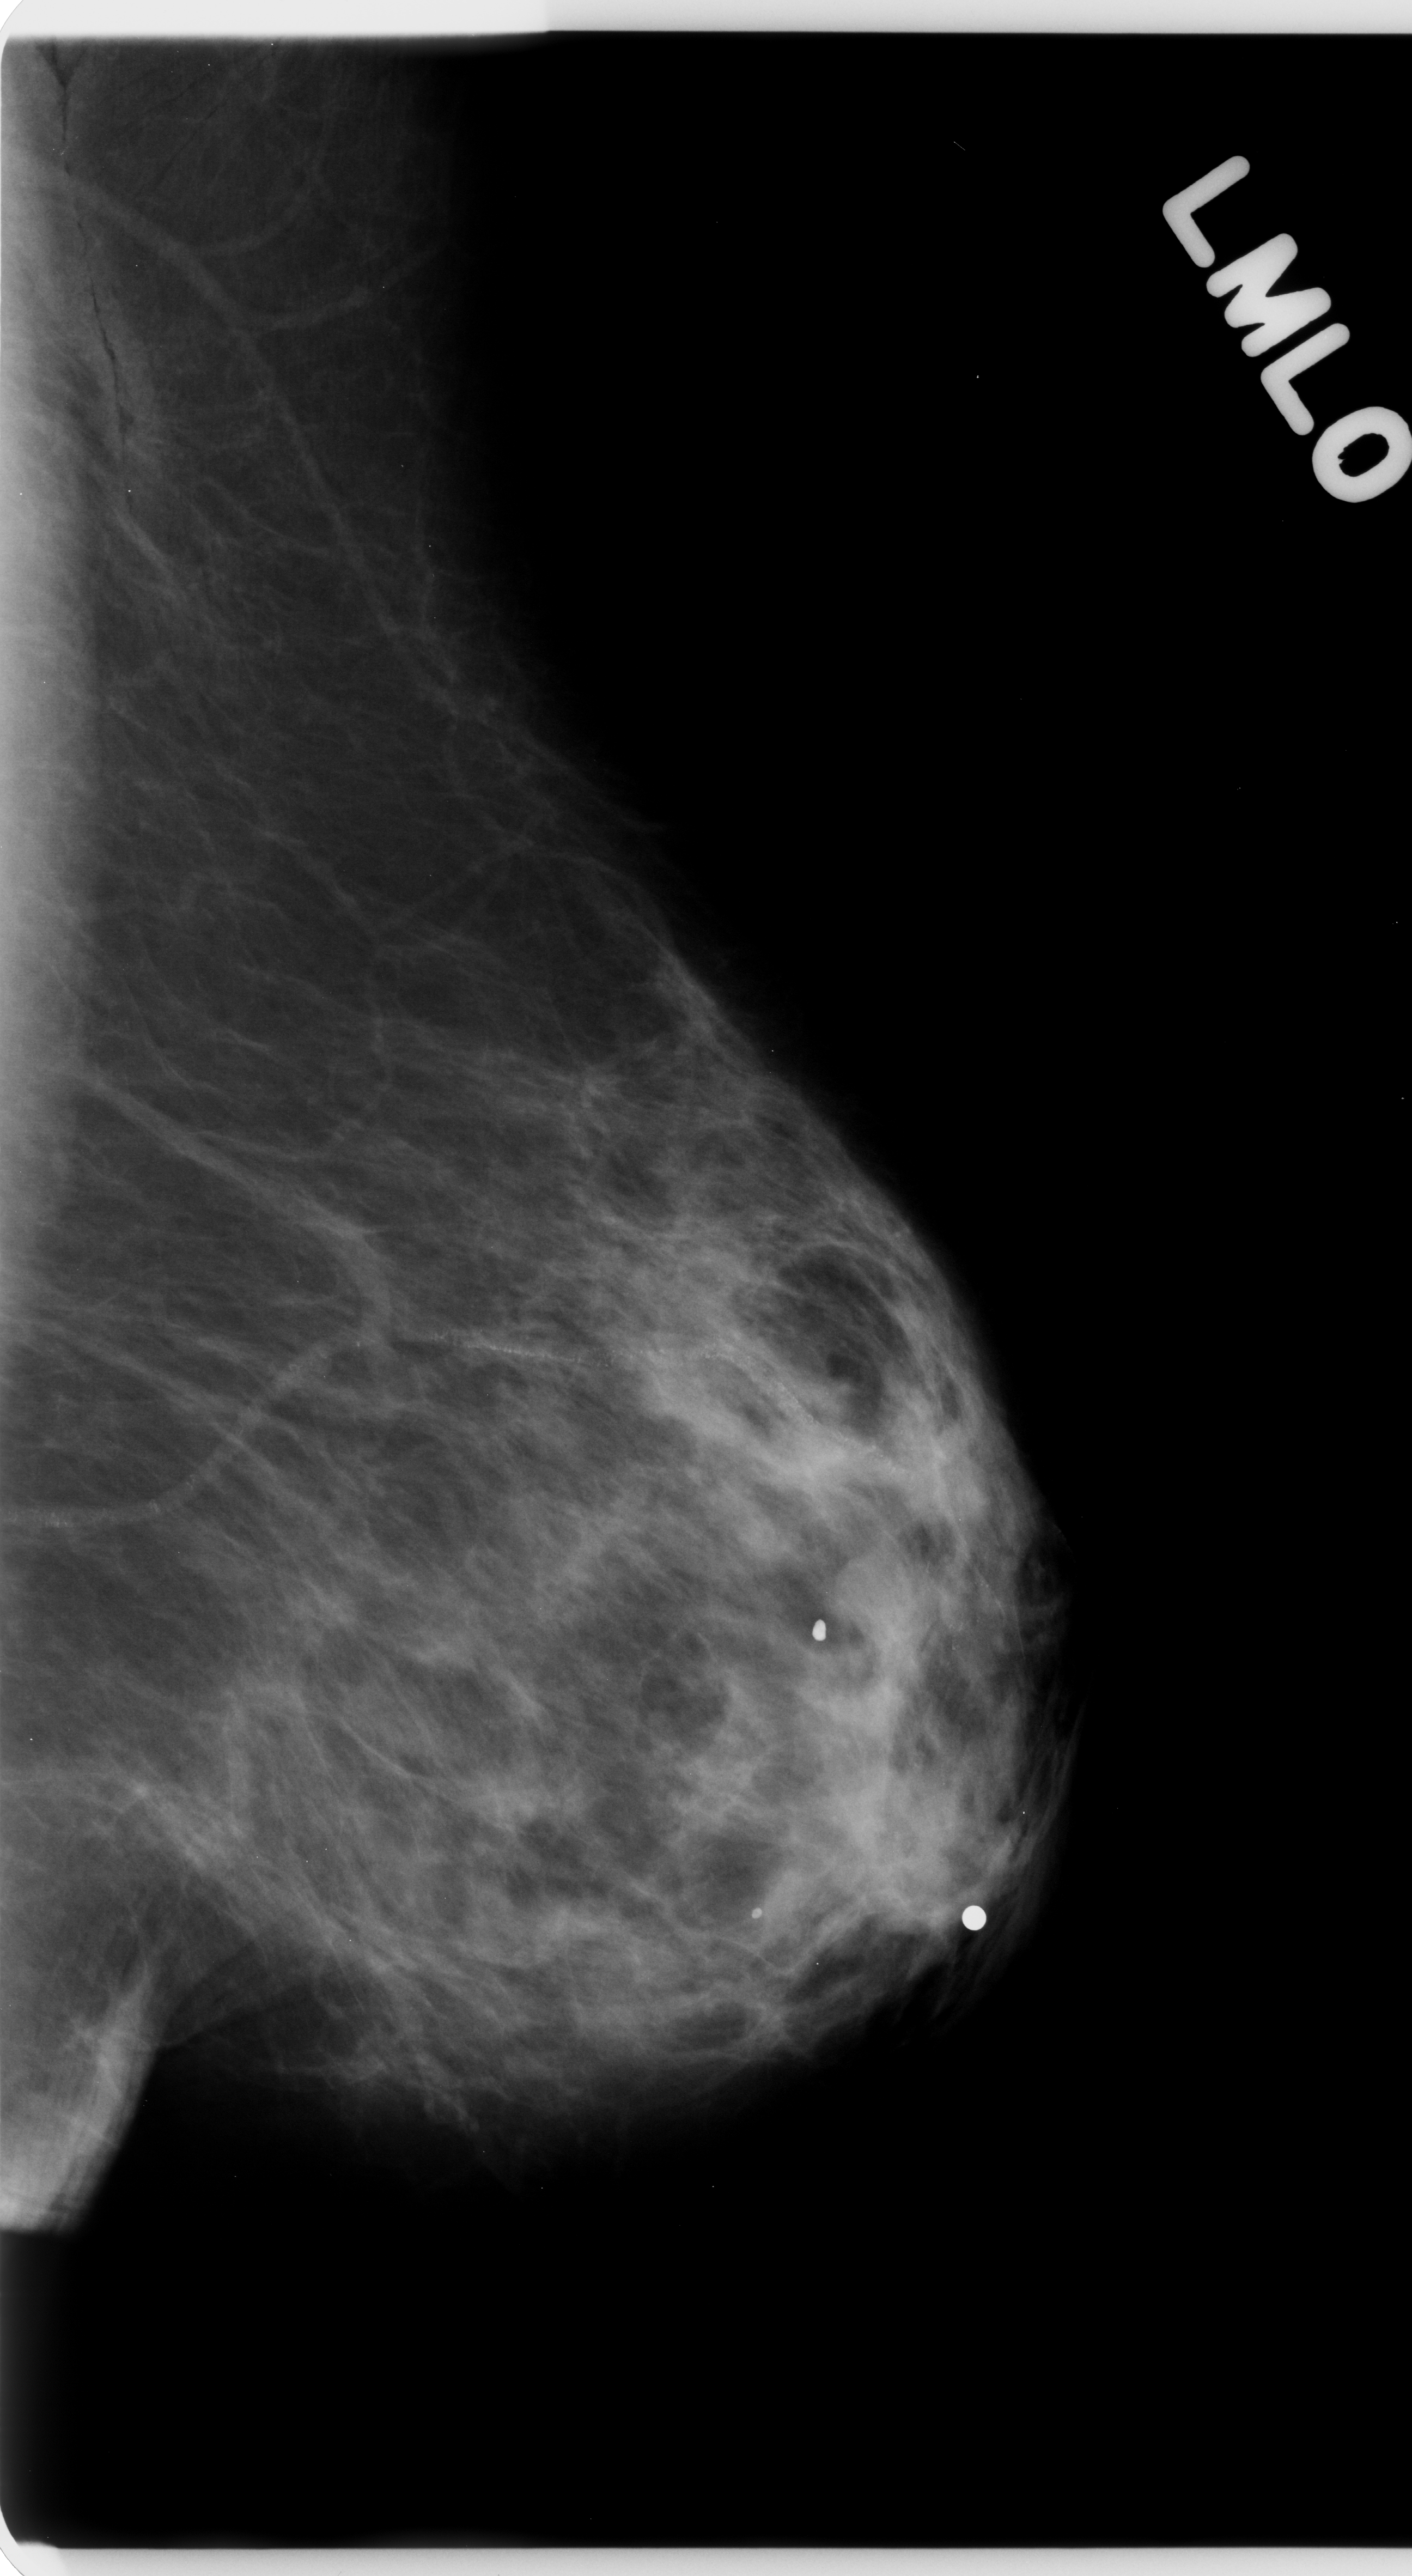
Mammogram (digitized film); left breast; mediolateral oblique (MLO) view; breast composition: scattered fibroglandular densities (BI-RADS density category 2 of 4).
- Marked abnormality: mass, shape lobulated, margins ill defined; BI-RADS assessment category 4; subtlety rating 3 on a 1 (subtle) to 5 (obvious) scale; pathology result (as recorded, not read from the image): malignant.